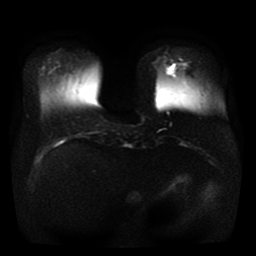
Breast MRI, one axial slice; diffusion-weighted series; image 2 of 4 stored at this slice position (different b-values; order by instance number); 1.5 T; 5 mm slice thickness; 256 × 256 image matrix, field of view 330 × 330 mm. Female patient.
Outlined on this slice (manually delineated by an expert):
- tumour on diffusion-weighted imaging: bounding box <168,66,174,72> (left, top, right, bottom; pixels)